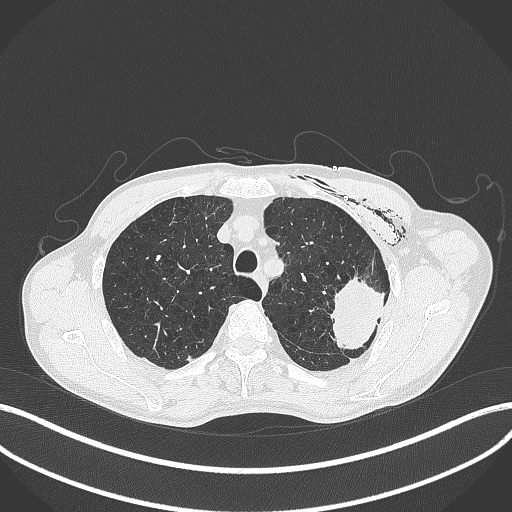
Chest CT, one axial slice; reconstruction kernel B70f; 120 kVp; lung window (W 1500 / L -600 HU); 1 mm slice thickness; 512 × 512 image matrix, field of view 400 × 400 mm. Male patient, age 58 years. Case-level facts recorded for this patient, not image findings: clinical TNM (as recorded): T3 N0 M0.
Annotated regions visible in this slice (bounding box drawn by a radiologist):
- lung tumour (recorded histology: adenocarcinoma): bounding box [x1, y1, x2, y2] px = [322, 272, 388, 356]